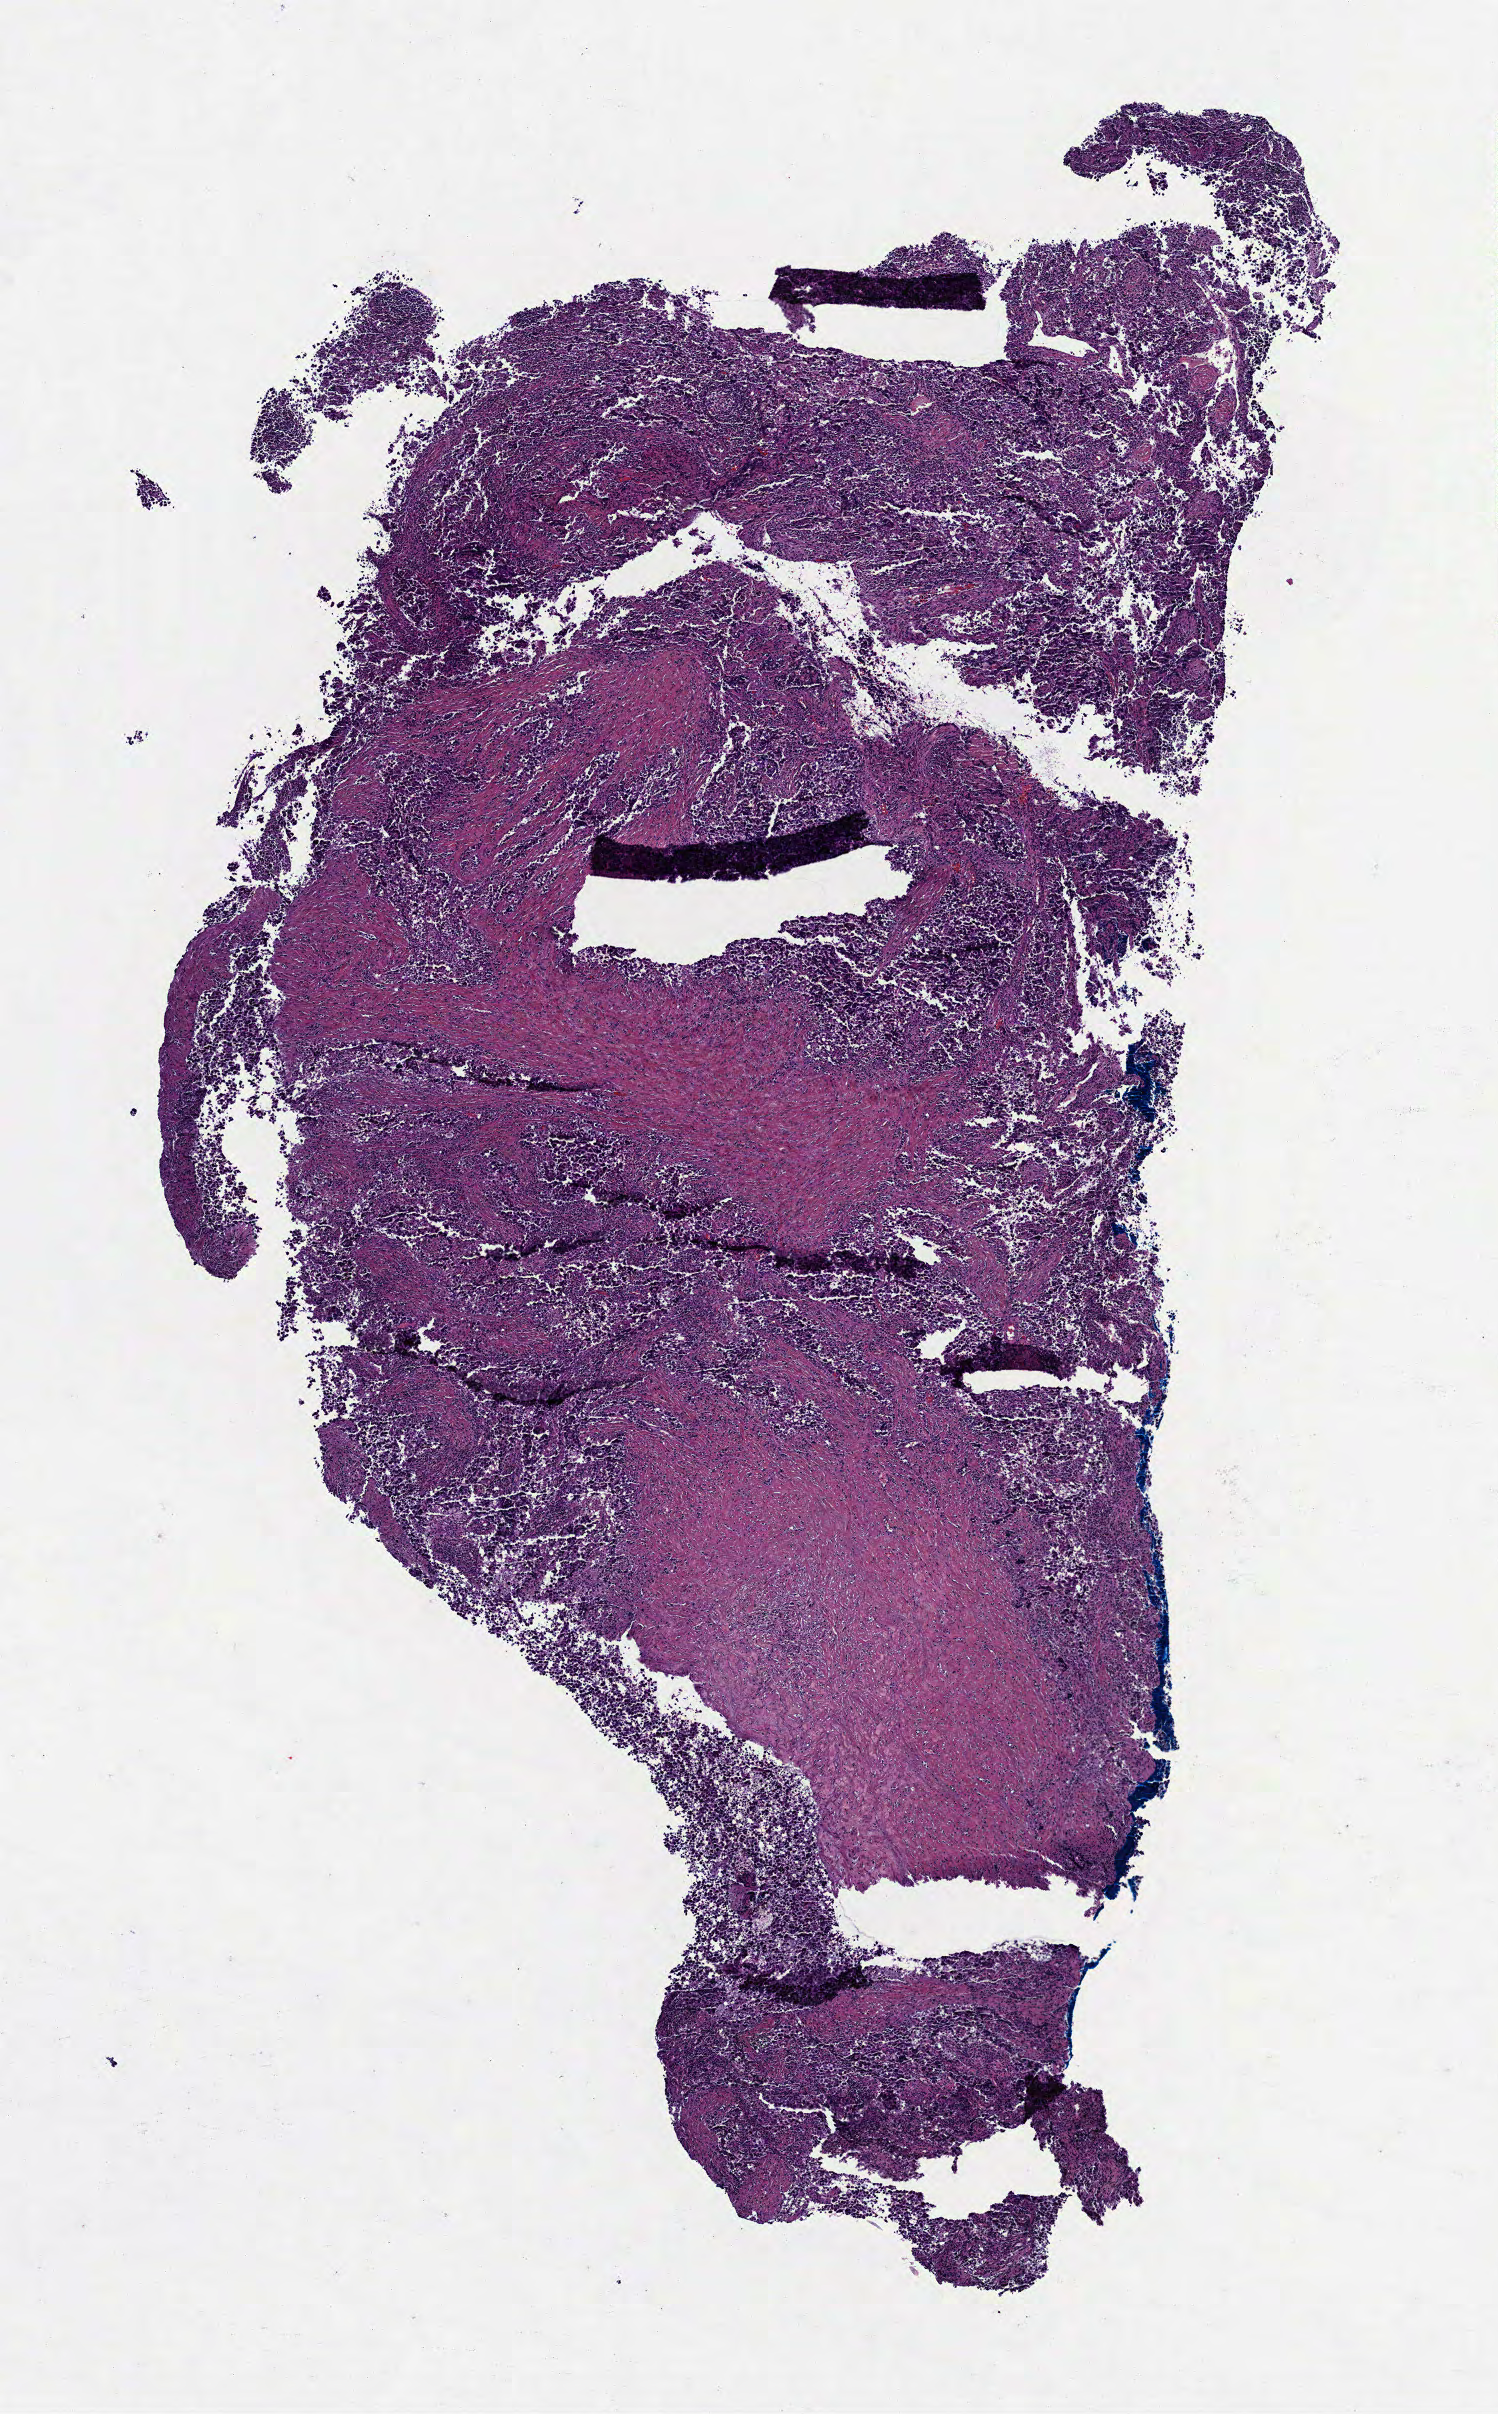
Whole-slide histology image, H&E-stained, a low-resolution overview of the entire scanned area, about 6.0 x 9.7 mm; formalin-fixed paraffin-embedded (FFPE) diagnostic section; testis, primary tumour sample. Male, age 38 years at initial diagnosis.
AJCC pathologic stage: IB. Diagnosis: Seminoma, NOS.